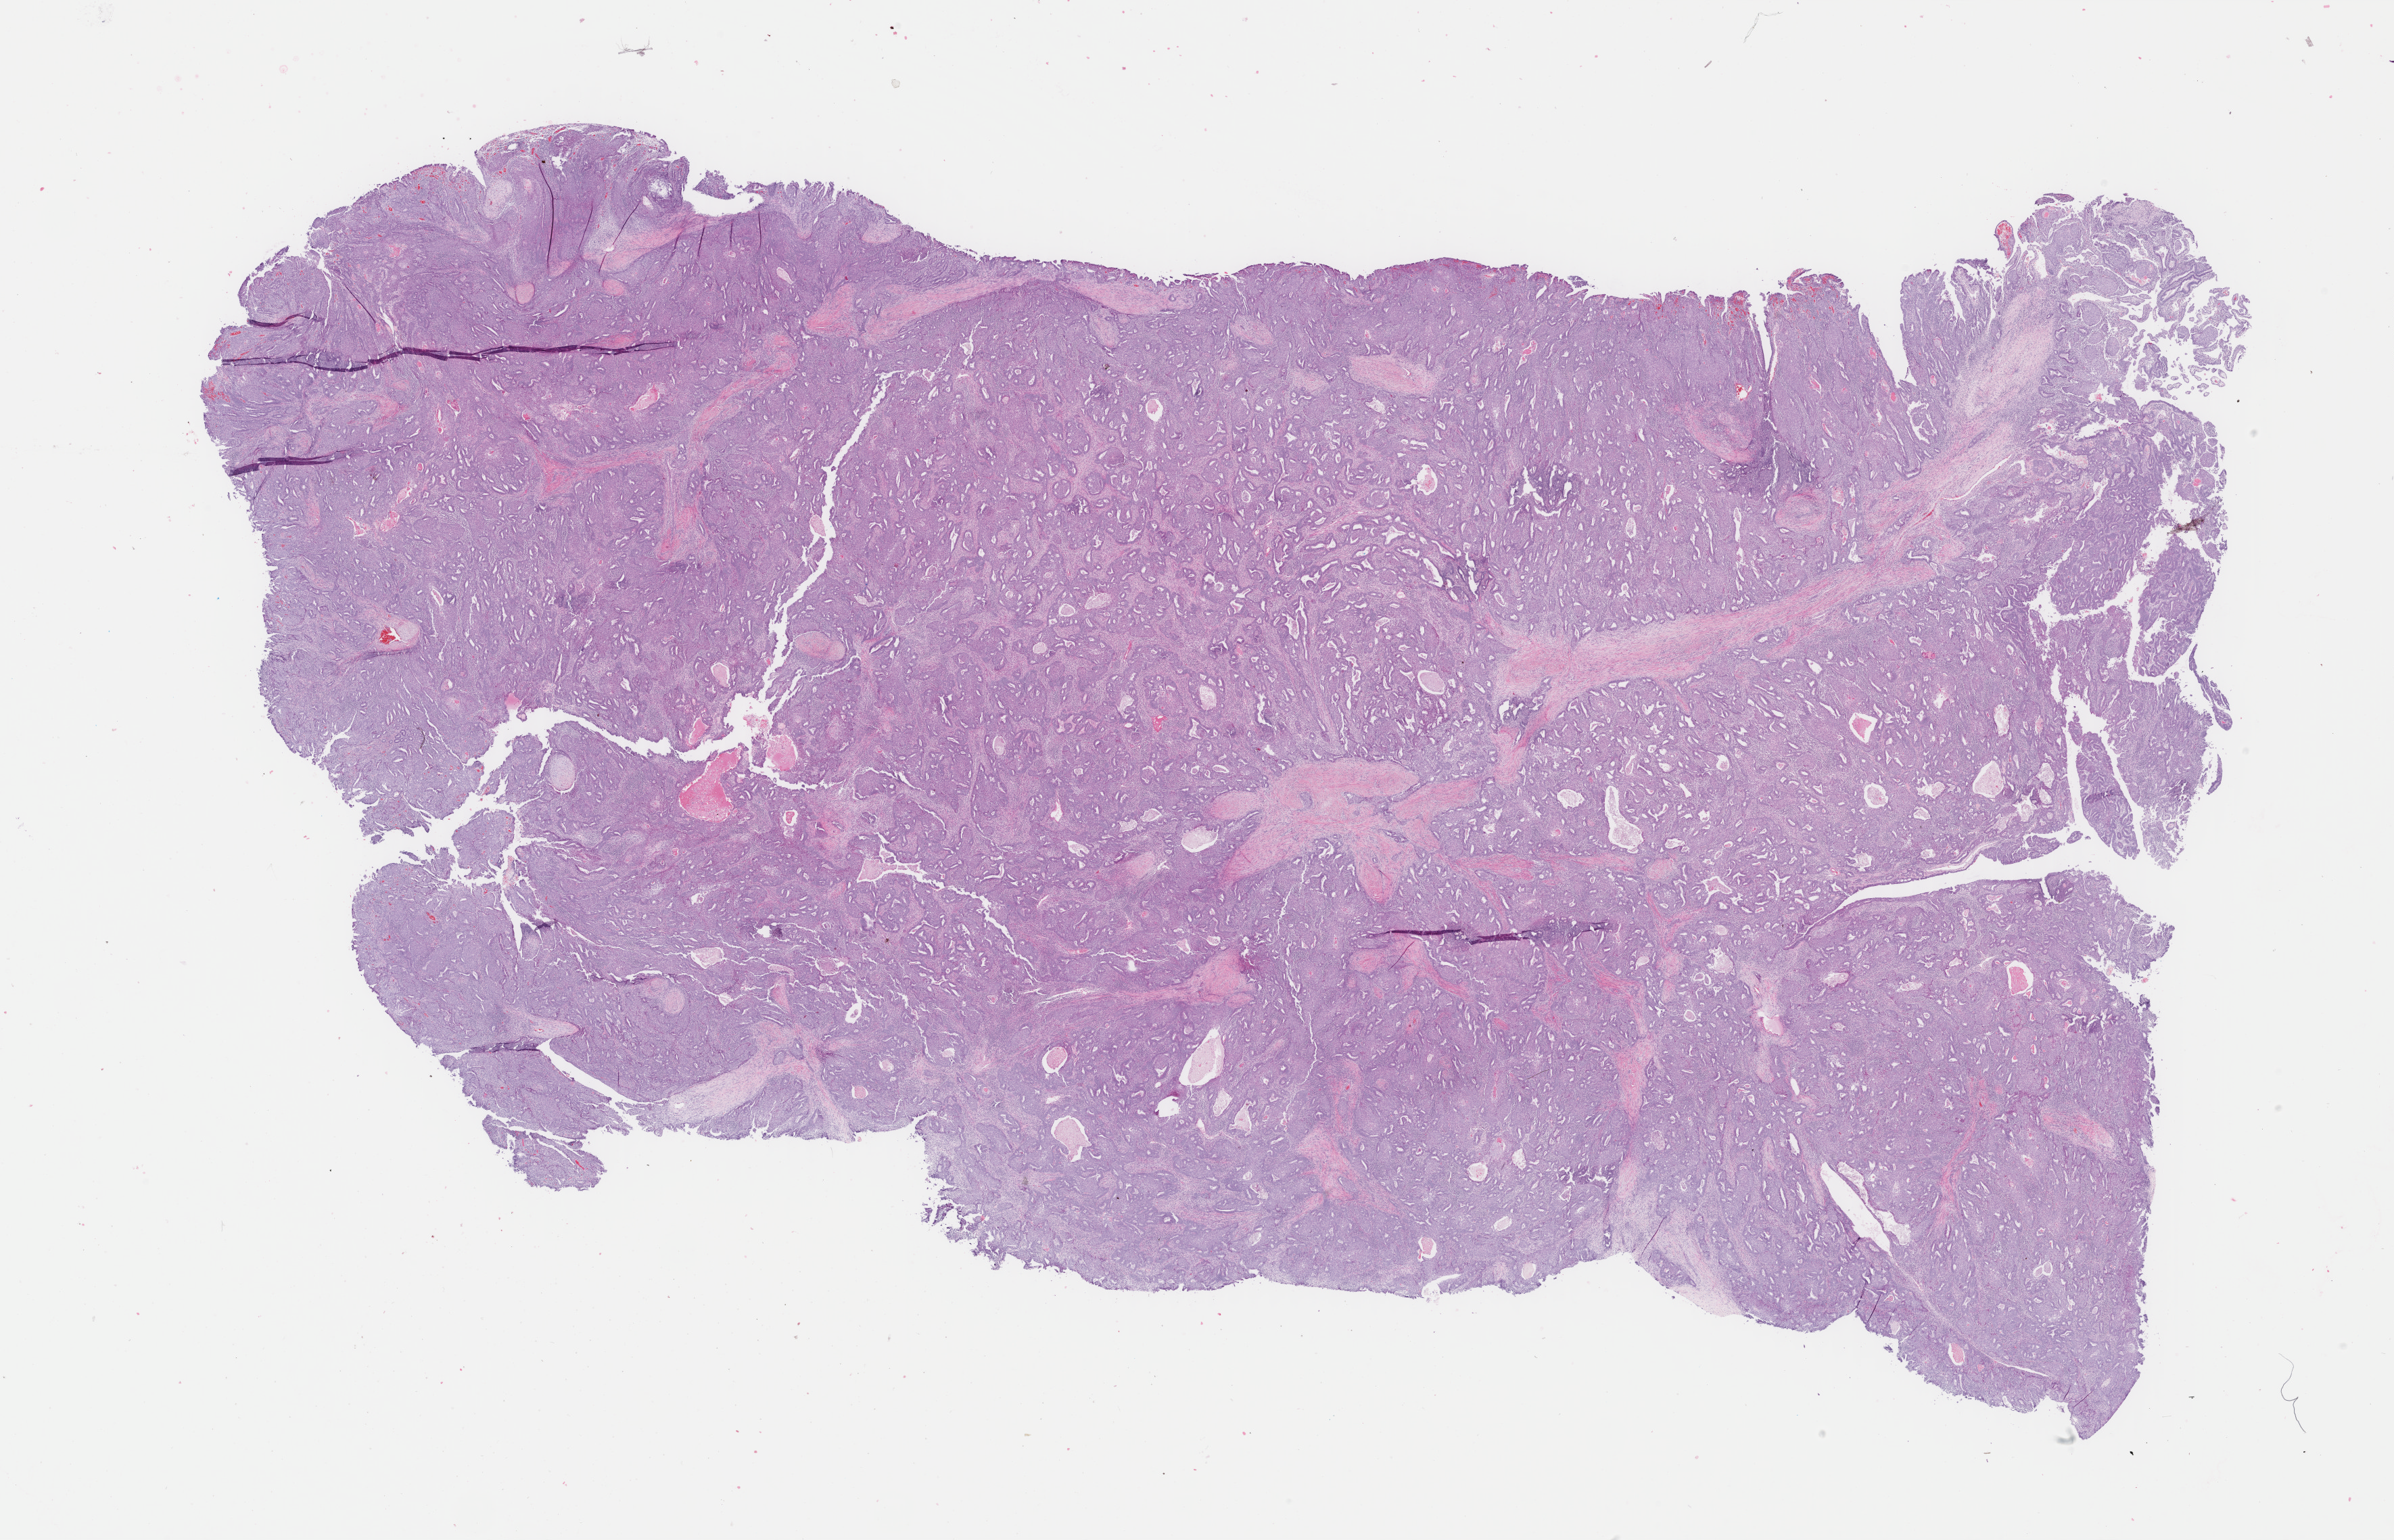
H&E-stained whole-slide image, low-resolution overview of the scanned area, about 28.1 x 18.1 mm (acquisition: 40x scan); FFPE section; sample: primary tumour, uterus. Female, age 48 years at initial diagnosis.
Histologic diagnosis: Endometrioid adenocarcinoma, NOS (endometrium).